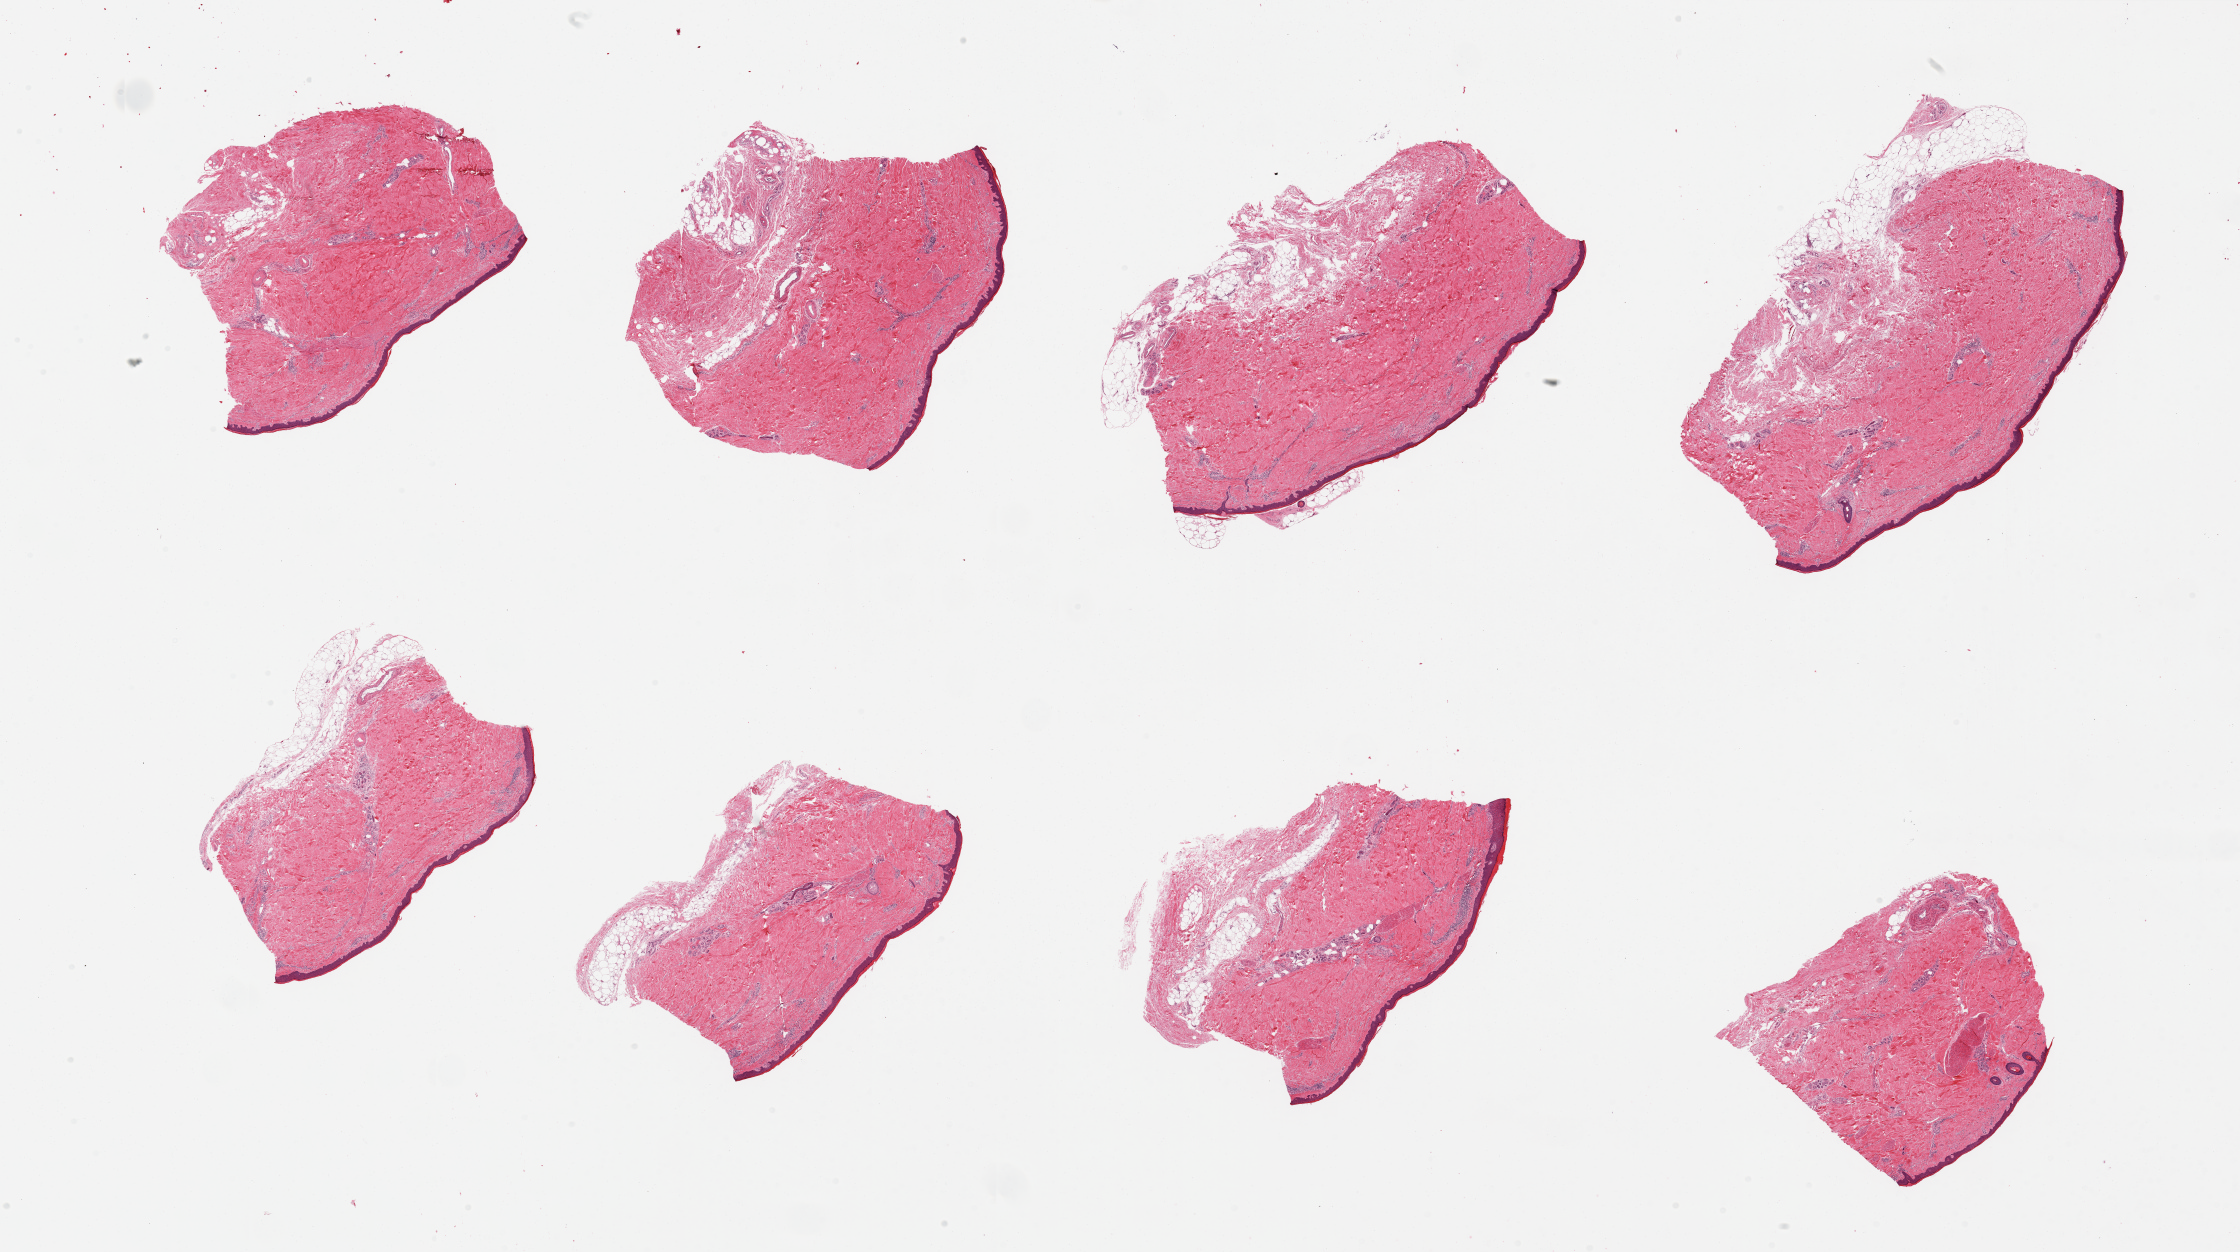
Whole-slide image, haematoxylin and eosin stain — a low-resolution overview of the entire scanned area, about 35.4 x 19.8 mm (slide scanned at 20x); PAXgene-fixed paraffin-embedded (PFPE) section; section of skin of lower leg (target tissue); tissue donor sample. Donor sex: male.
Reviewer comment on this tissue sample: 8 pieces, minimal dermal fat; squamous epithelium is 60-70 microns.